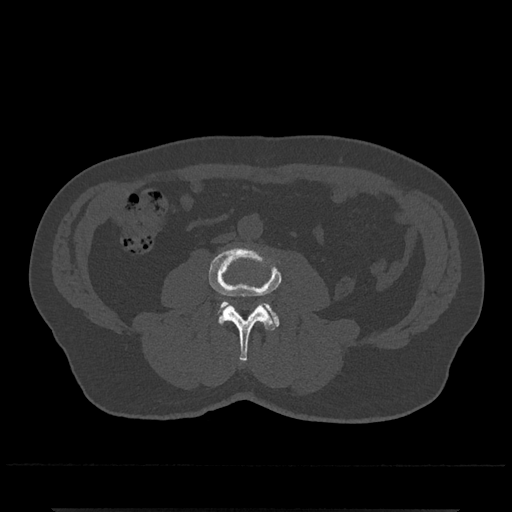
CT including the spine, one axial slice. Position 206 of 797 along the scan axis. Reconstruction kernel Br40s/3. Bone window (W 1800 / L 400 HU). 0.5 mm slice thickness. 512 × 512 image matrix, field of view 393 × 393 mm. Patient: male, 67 years. From the clinical record (not read from this slice): primary cancer: prostate.
Outlined on this slice (semi-automatic segmentation, software-assisted and operator-edited):
- L3 vertebra: bounding box [x1, y1, x2, y2] px = [208, 246, 282, 361]
- L4 vertebra: [220, 301, 279, 326]